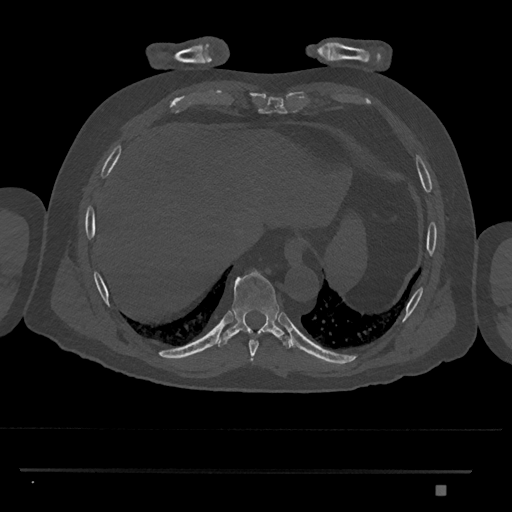
CT including the spine, one axial slice. Slice 1074 of 1134 in the series (ordered by position). 120 kVp. Bone window (W 1800 / L 400 HU). 512 × 512 image matrix. Patient: male, 65 years. From the clinical record (not read from this slice): primary cancer: prostate.
Annotated regions visible in this slice (semi-automatically segmented with operator editing):
- T8 vertebra: bounding box <249,340,259,356> (left, top, right, bottom; pixels)
- T9 vertebra: <216,270,293,349>